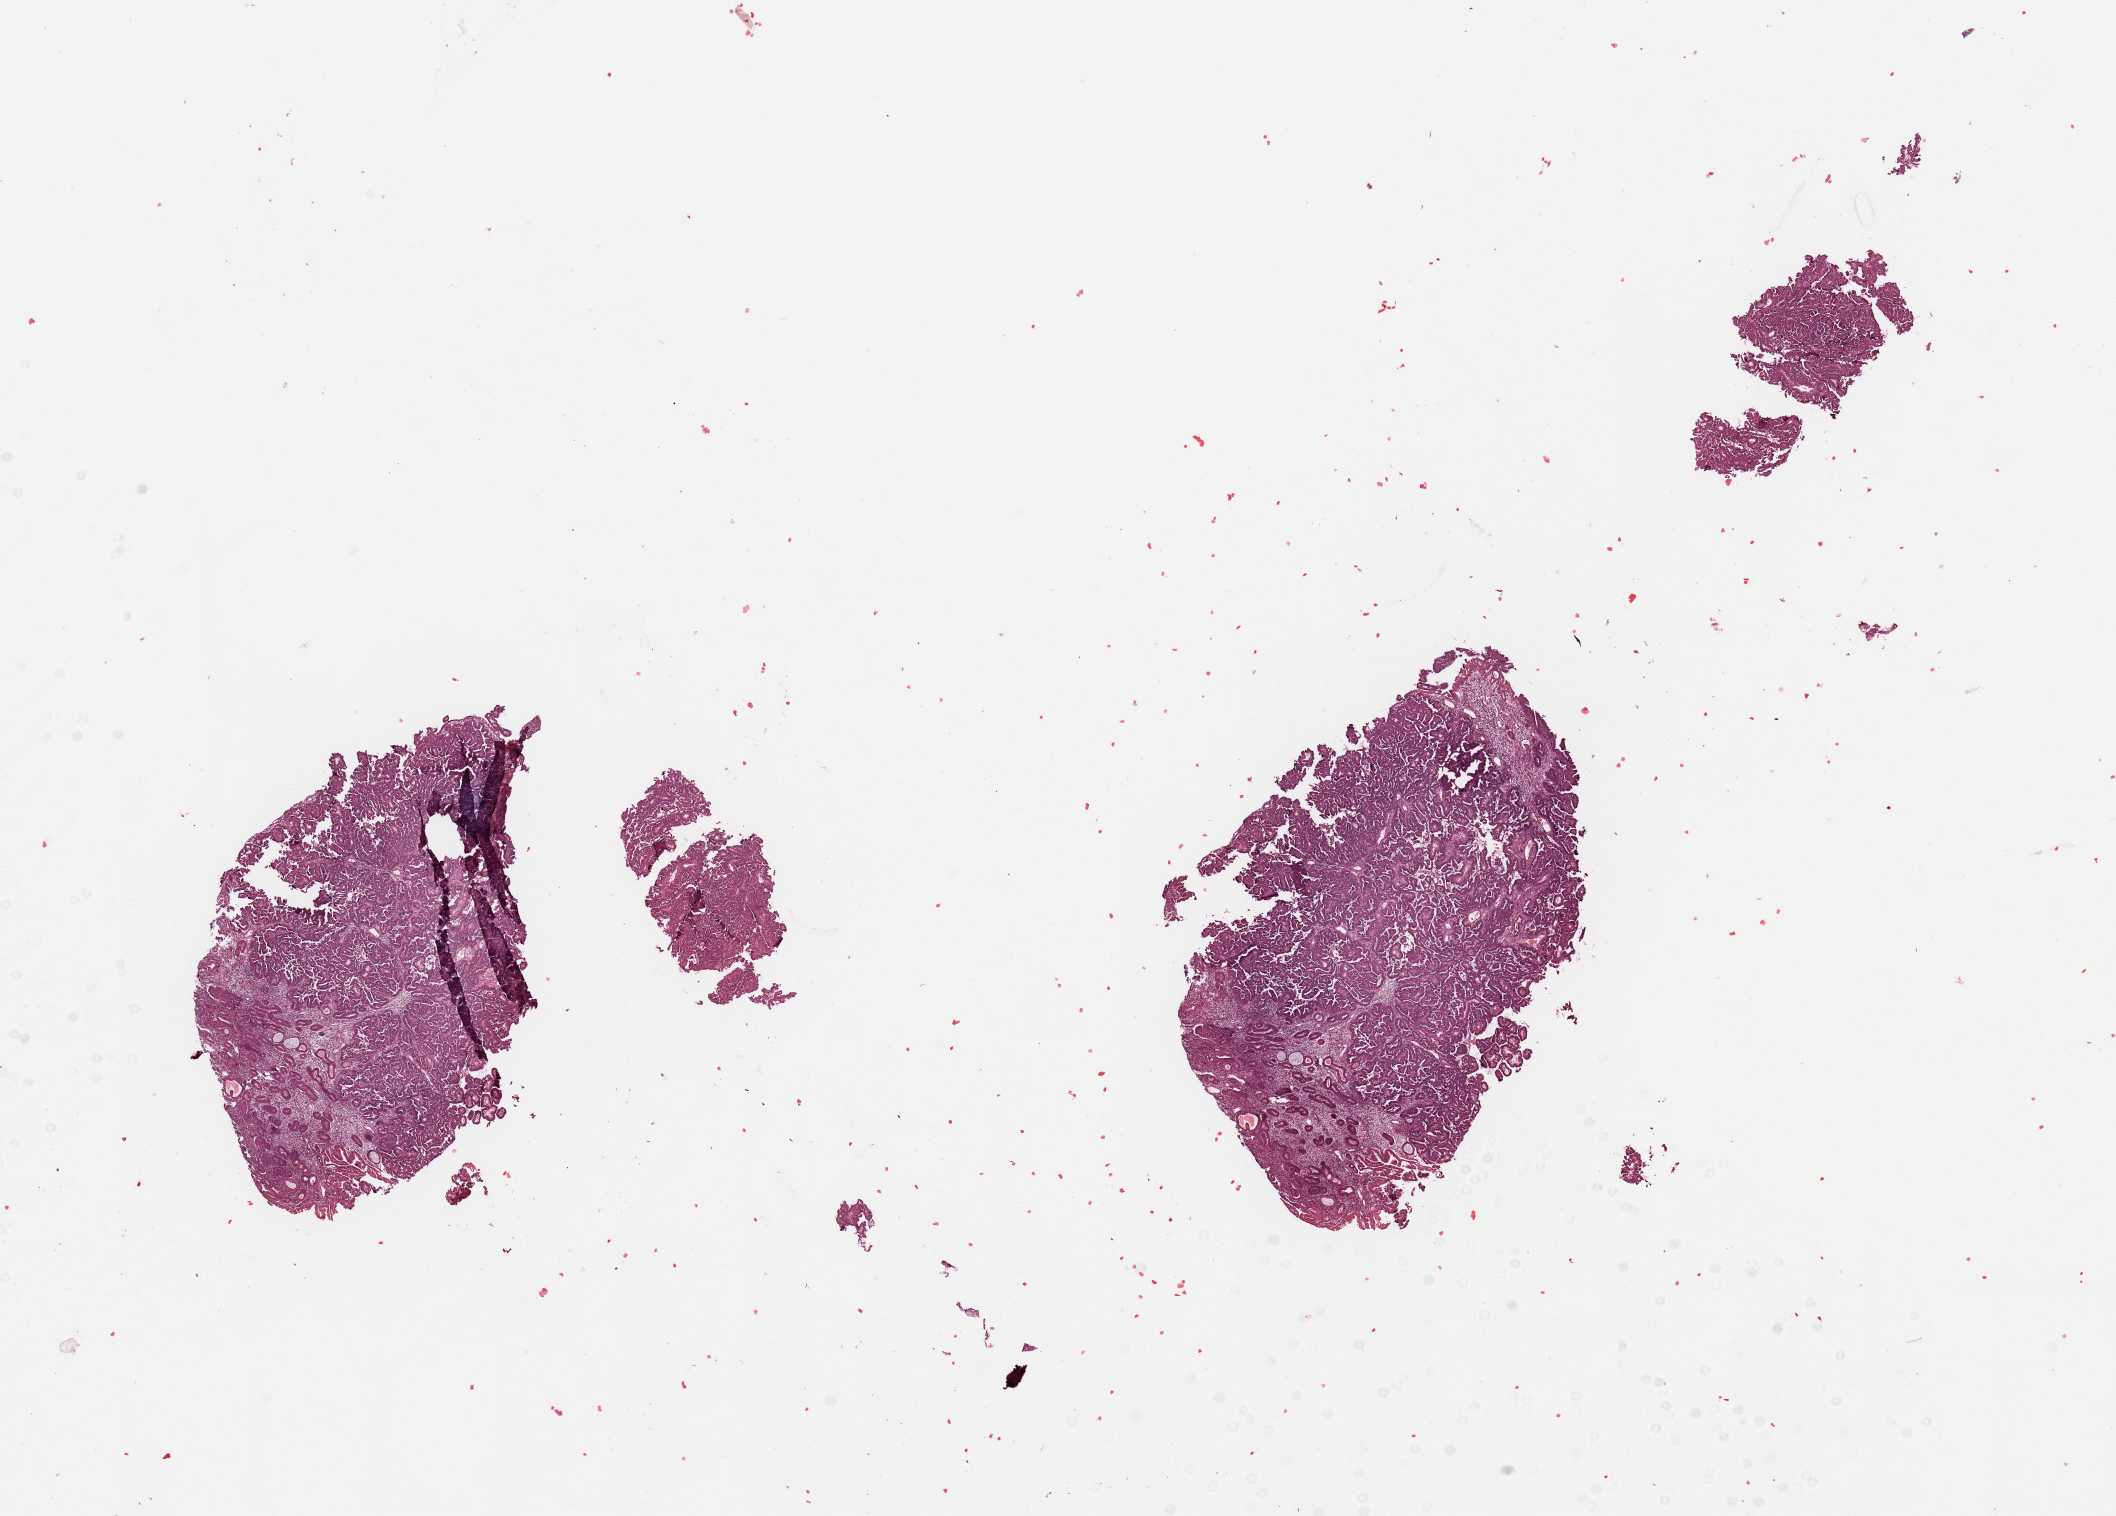
Whole-slide histology image, H&E, a low-resolution overview of the entire scanned area, about 16.7 x 12.0 mm, tumour tissue sample, sampled site: uterus. Female, 73 y/o. Histologic grade: G3 (poorly differentiated). Pathologist review of this section (percent, as recorded): tumour nuclei 80%, necrosis 0%.
• diagnosis: Endometrioid adenocarcinoma, NOS
• primary tumour site (as recorded): anterior endometrium
• AJCC pathologic stage: IVB